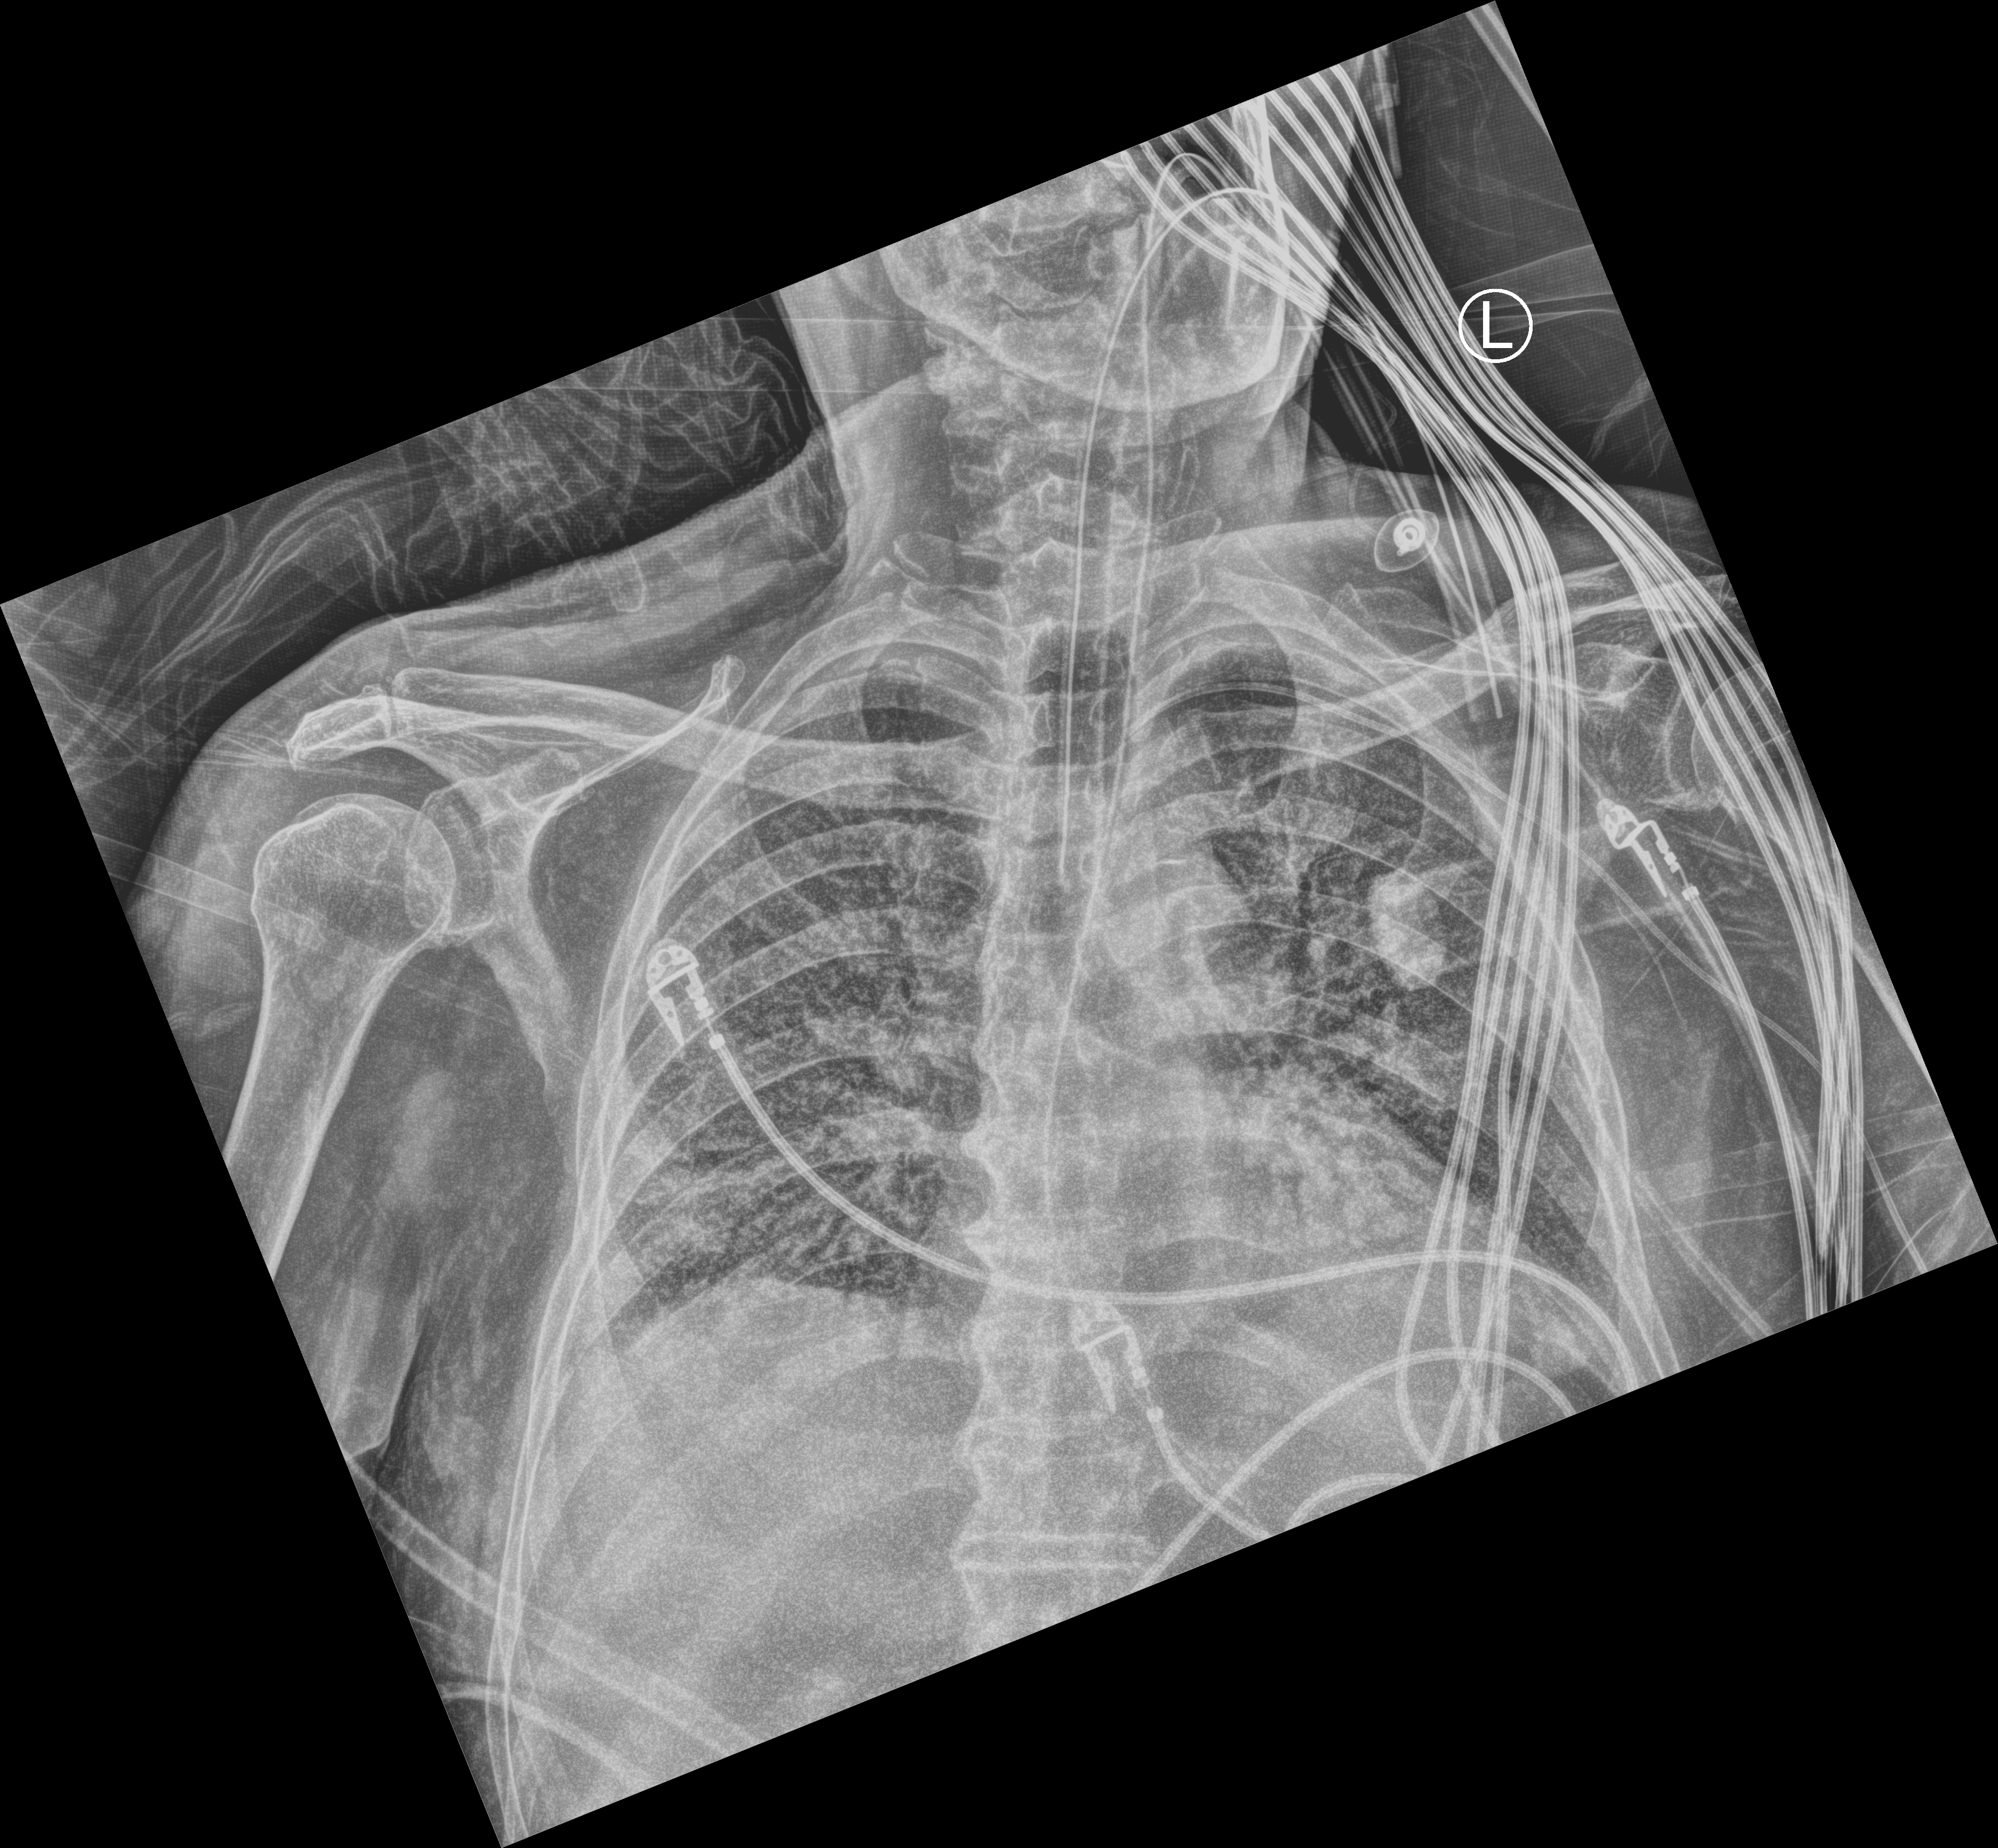
Chest X-ray (portable). Male patient hospitalised with COVID-19, age 75–90 years.
Admission-level facts for this patient (not findings on this image; timing relative to this image not recorded): admitted to intensive care during this hospital stay: yes; mechanically ventilated during this hospital stay: yes.